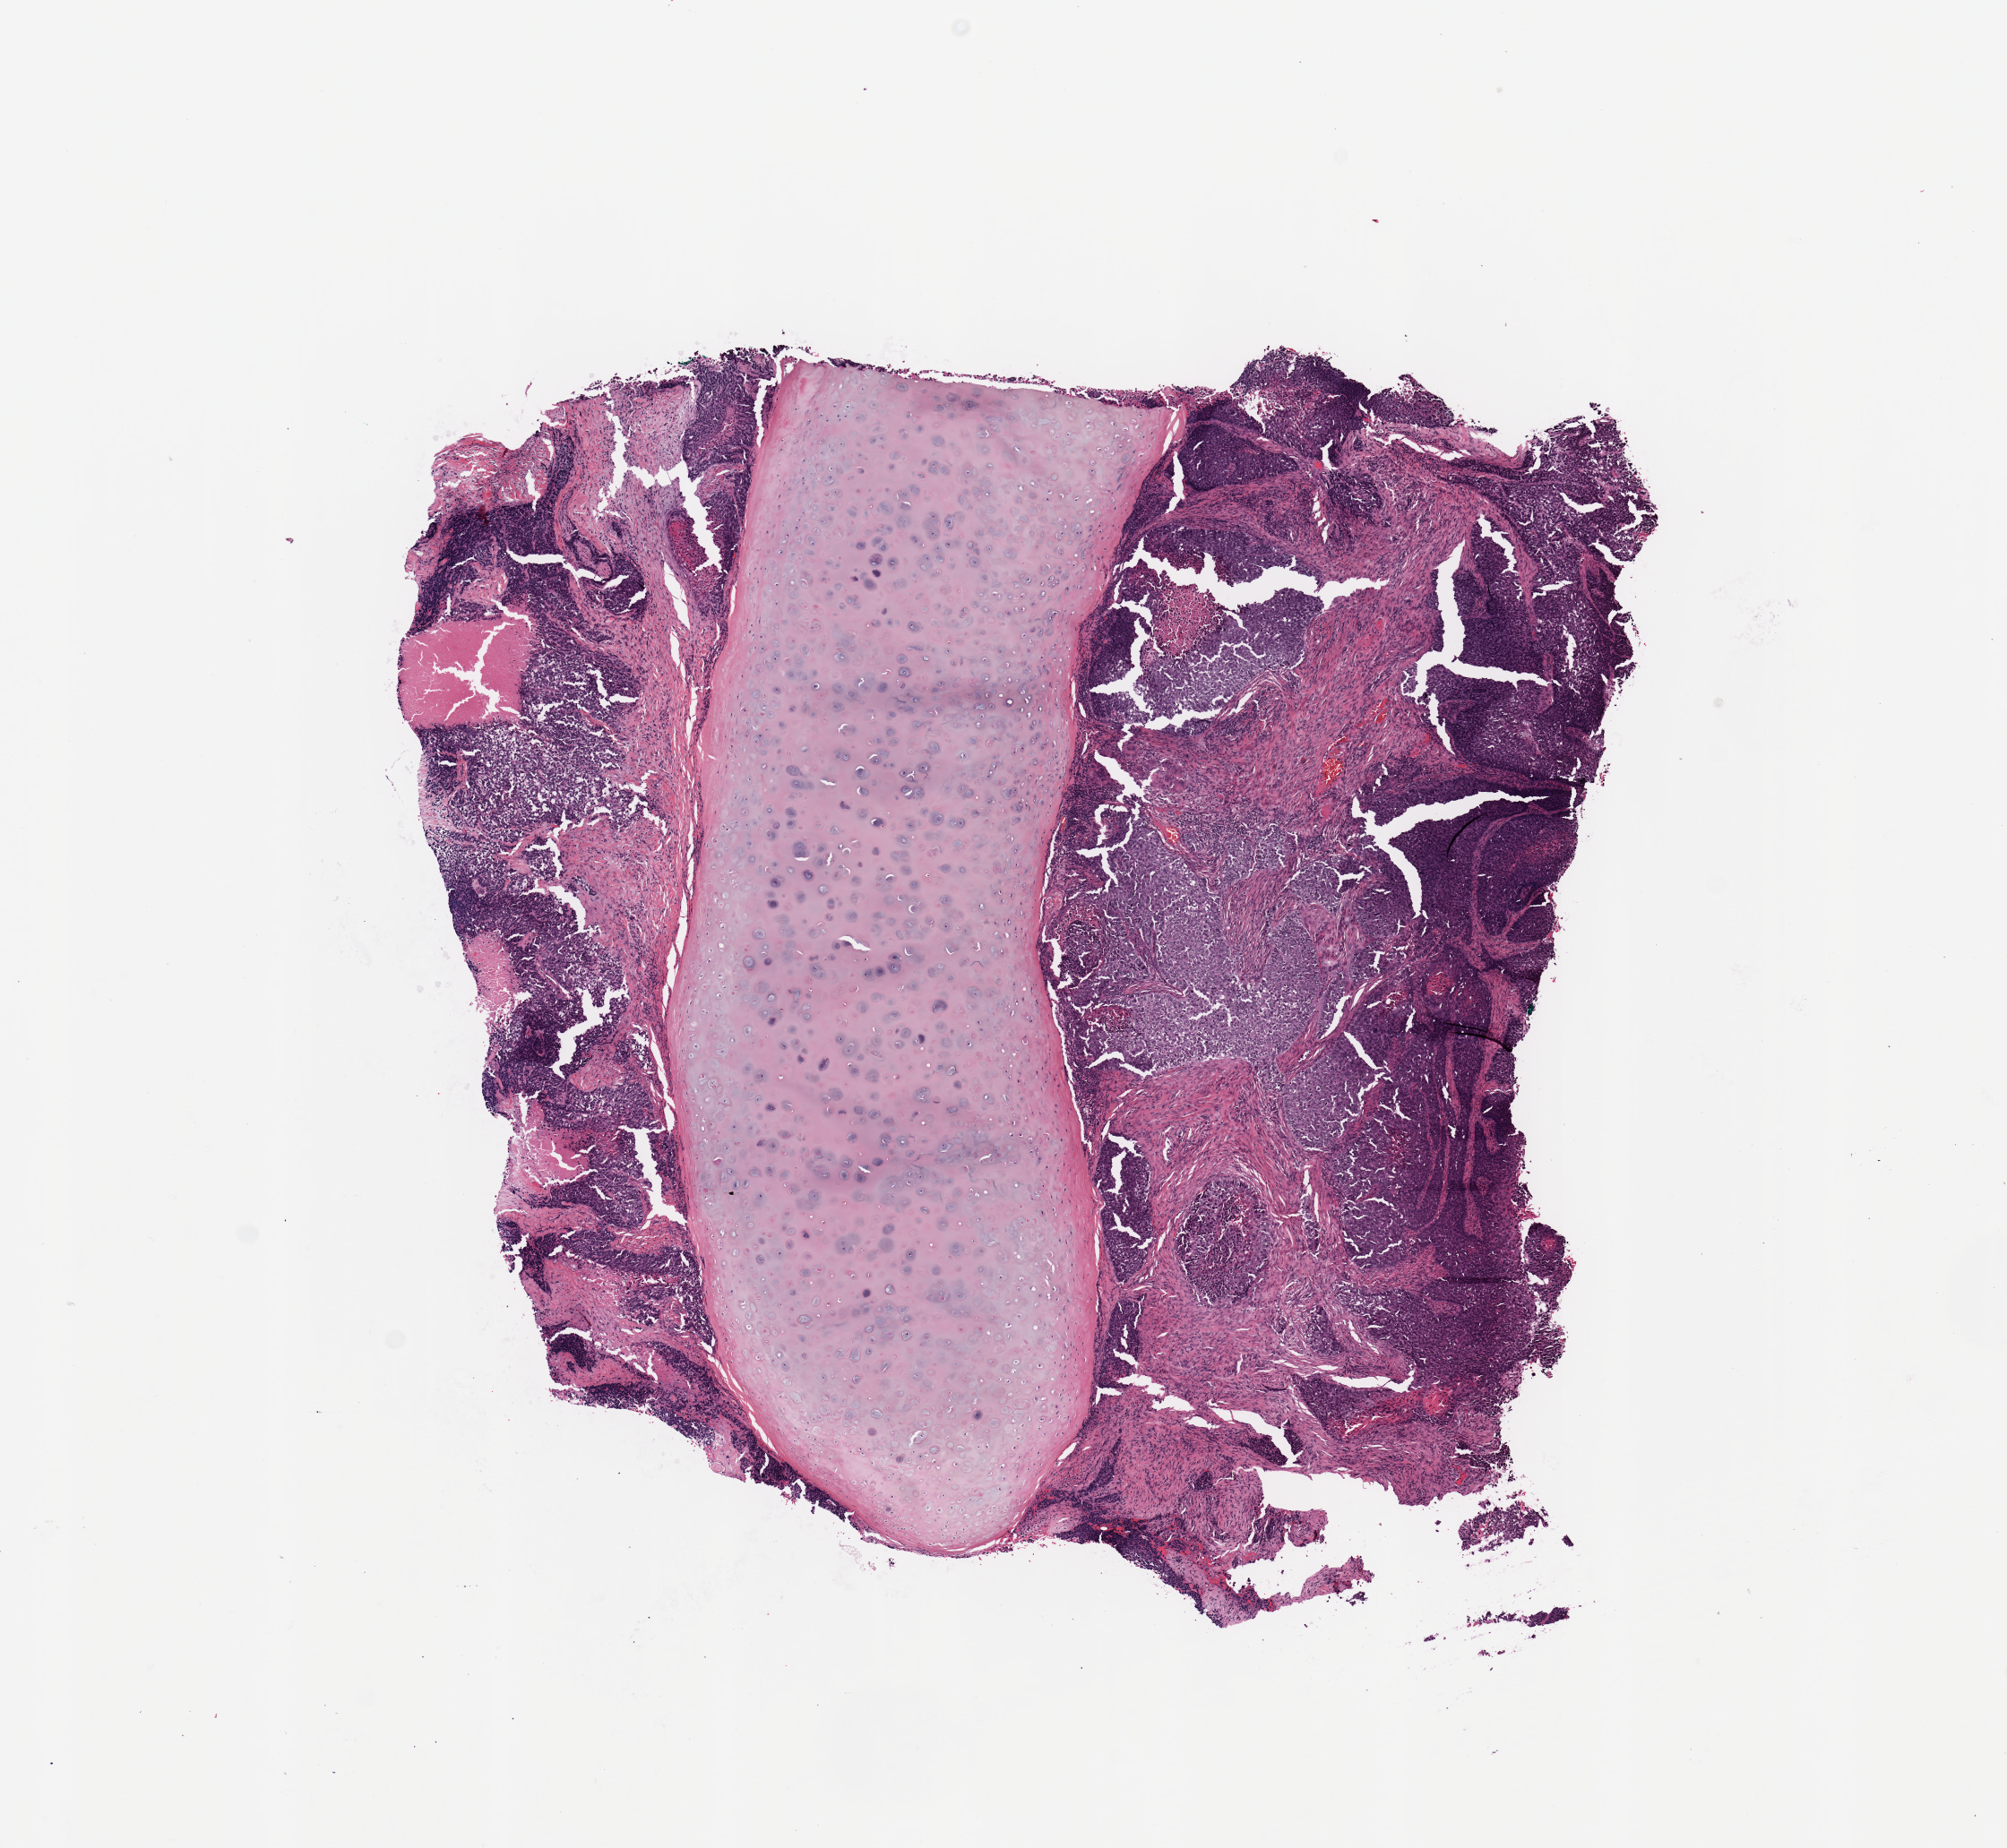
Digitized Hematoxylin and eosin (H&E) stained tissue section (whole slide), a low-resolution overview of the entire scanned area, about 8.9 x 8.2 mm; tumour tissue sample, lung. Male, 63 y/o. Histologic grade: G2 (moderately differentiated).
Primary tumour site (as recorded): right upper lobe. AJCC pathologic stage: IIA. Diagnosis: Squamous cell carcinoma, NOS.